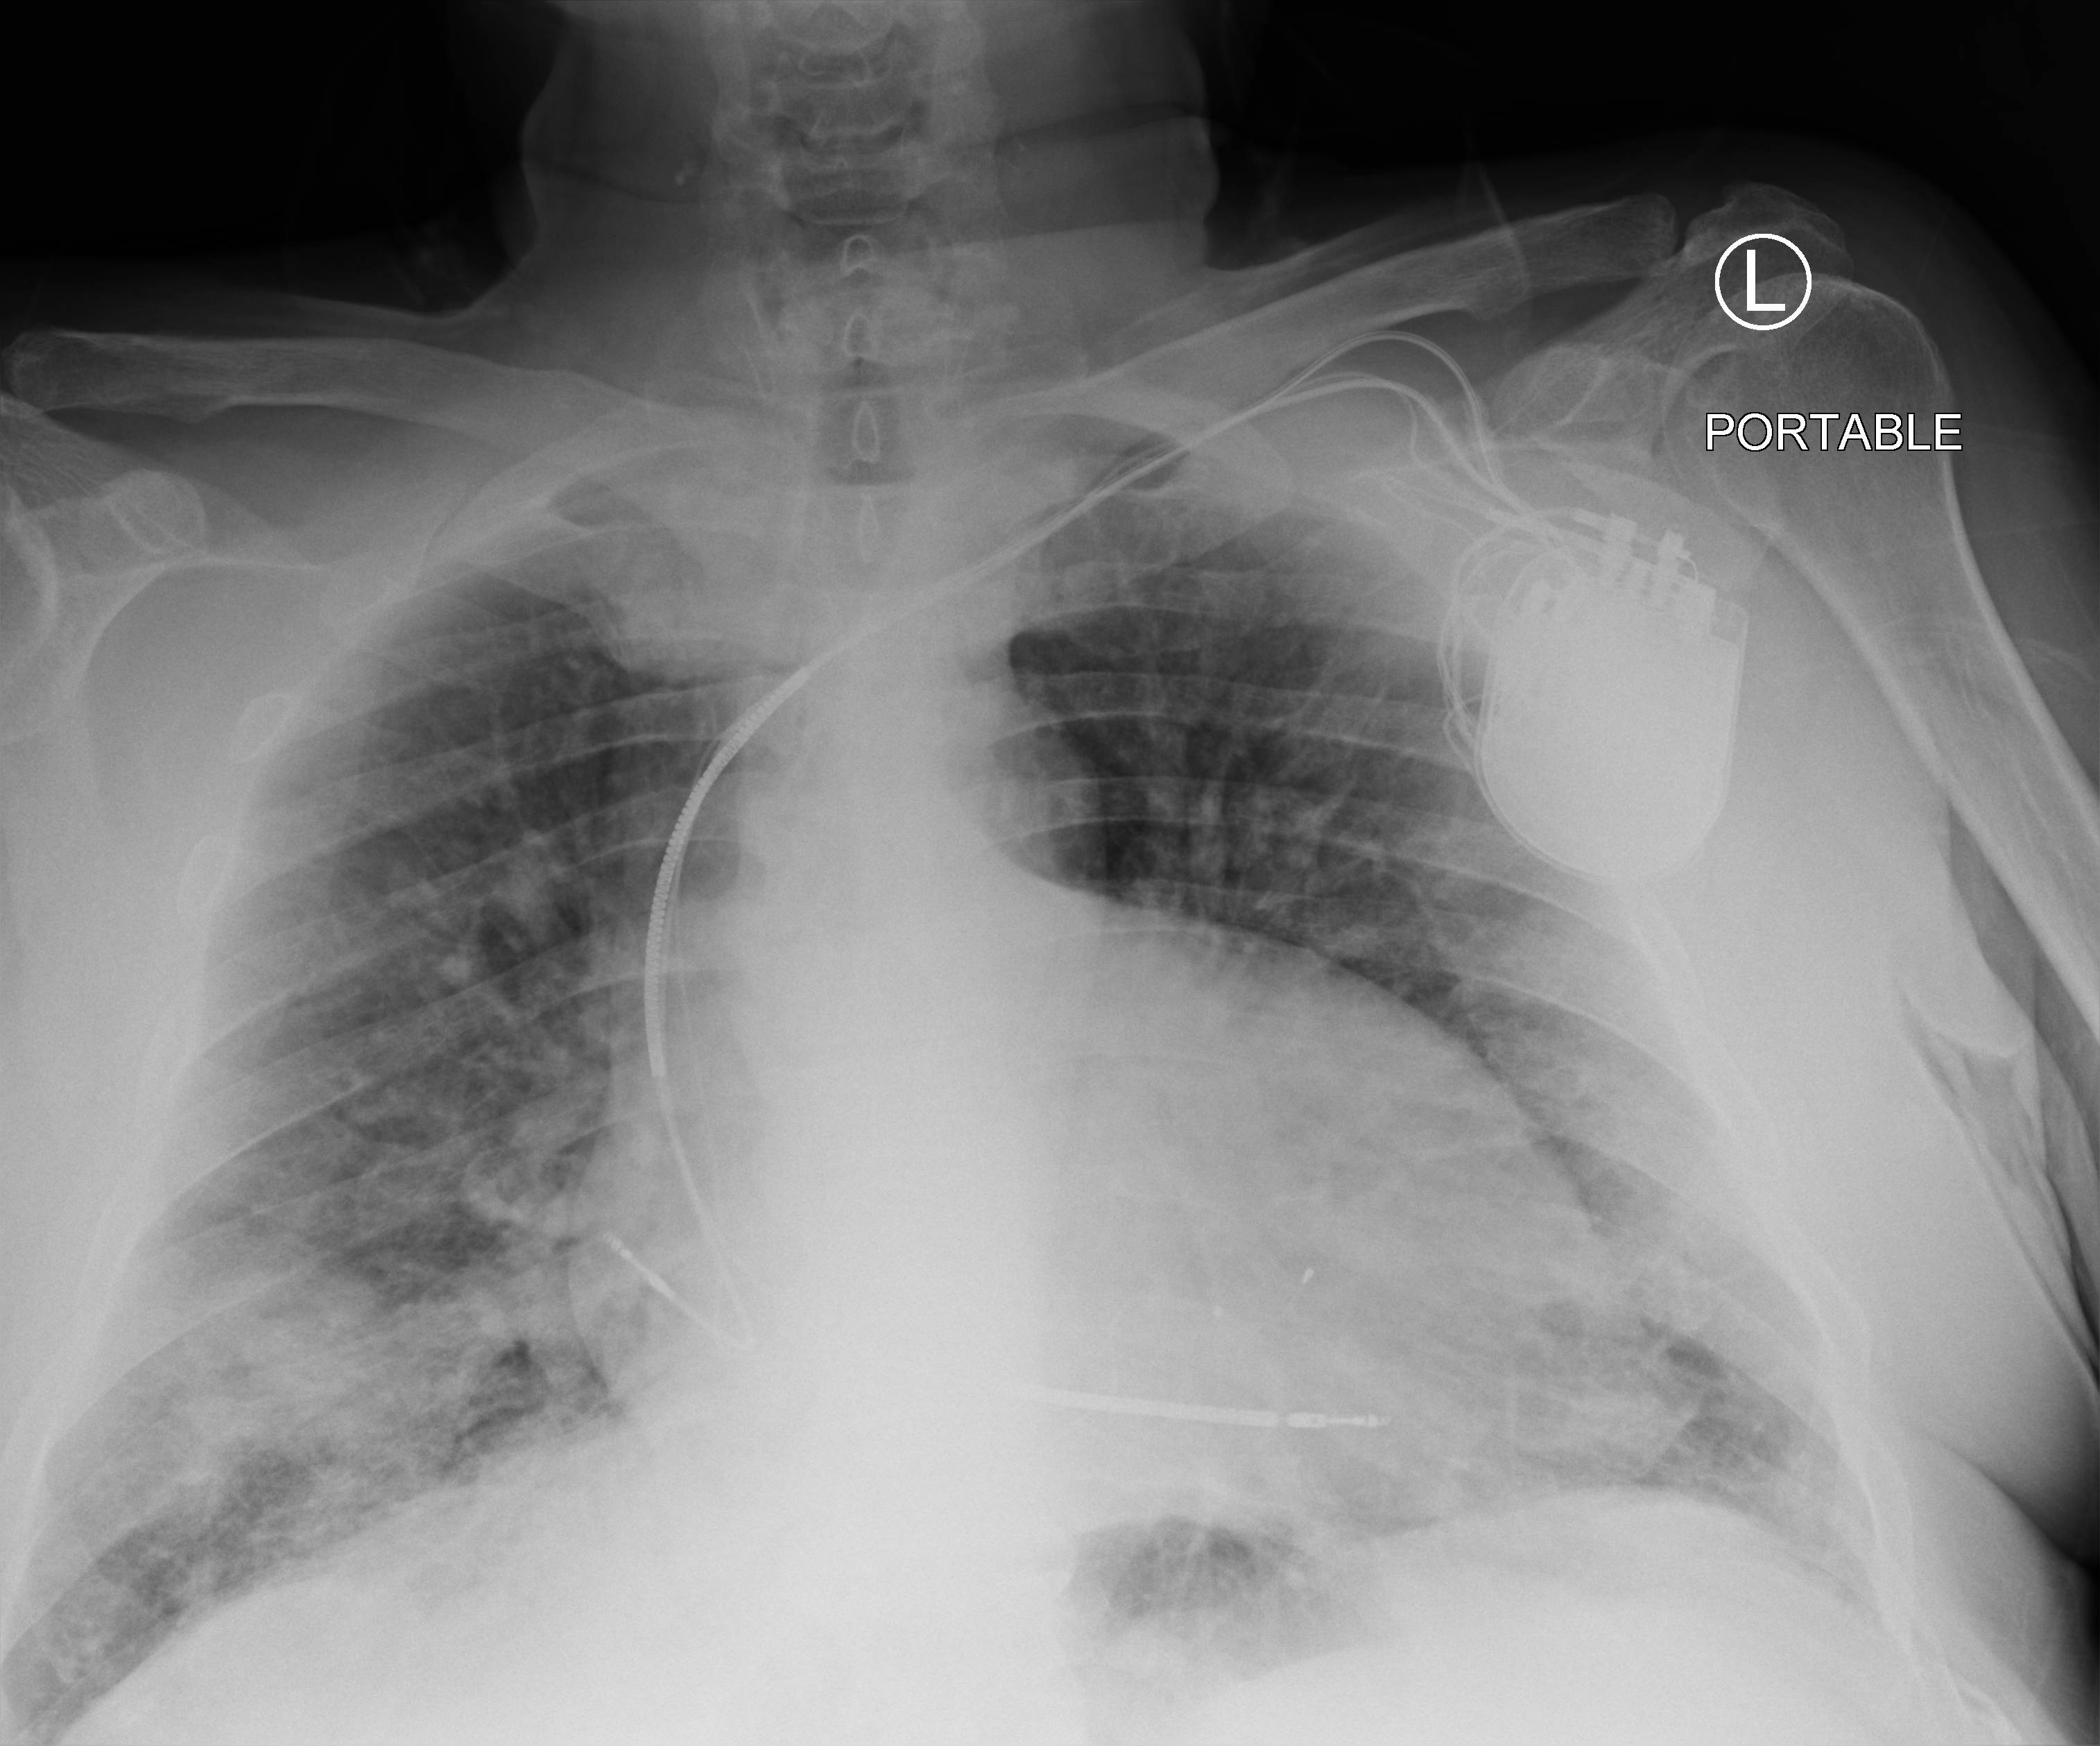
Portable chest radiograph. Patient hospitalised with COVID-19; male, aged 60–74 years.
Hospital-stay facts (about this admission, not read from this image; timing relative to this image not recorded):
- other chronic lung disease (admission record): no
- length of hospital stay: 27 days